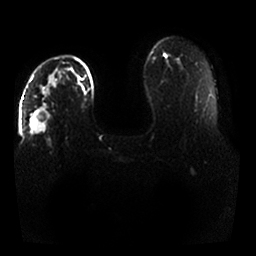
Breast MRI, one axial slice. Position 20 of 25 along the scan axis. Diffusion-weighted series; image 2 of 4 stored at this slice position (different b-values; order by instance number). 1.5 T. 256 × 256 image matrix. Female patient.
Annotated regions visible in this slice (expert manual segmentation):
- tumour on diffusion-weighted imaging: bounding box (x1, y1, x2, y2) in pixels: (30, 74, 58, 133)